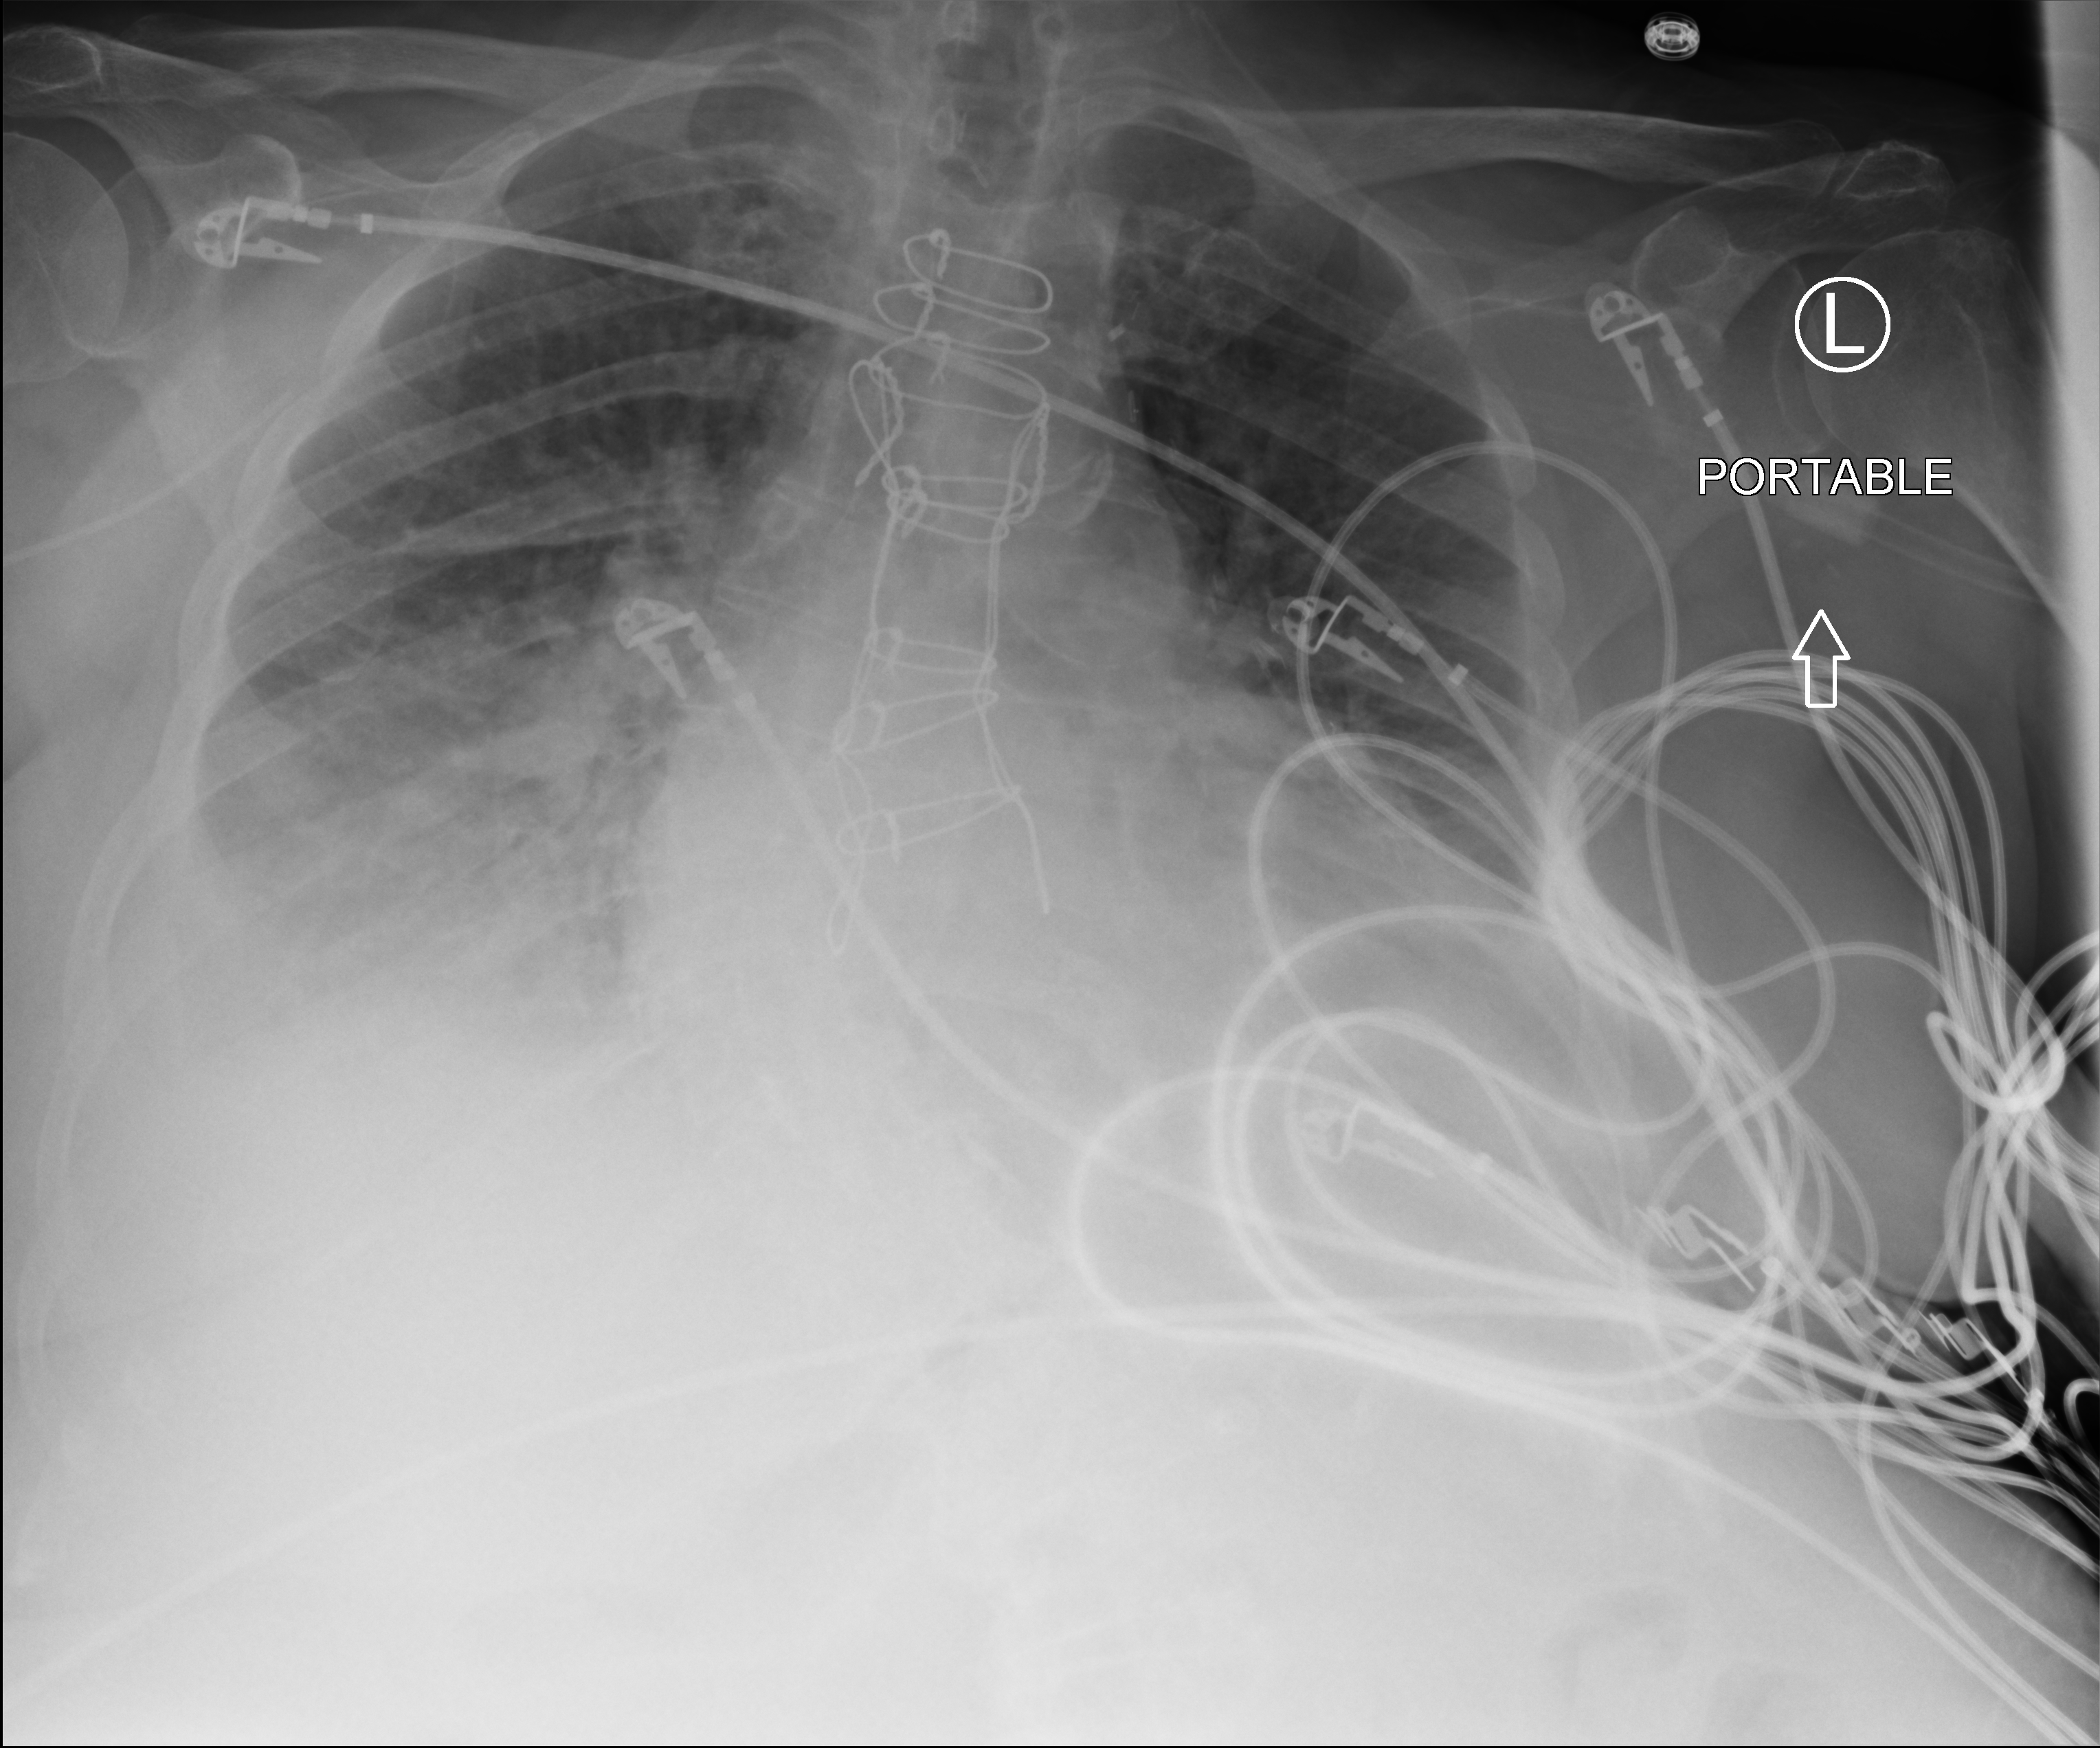
Portable chest radiograph, anteroposterior (AP) projection. Female patient hospitalised with COVID-19, age 75–90 years.
From the hospital-stay record, not from the radiograph (when in the stay this image was taken is not recorded): mechanically ventilated during this hospital stay: no; admitted to intensive care during this hospital stay: no.